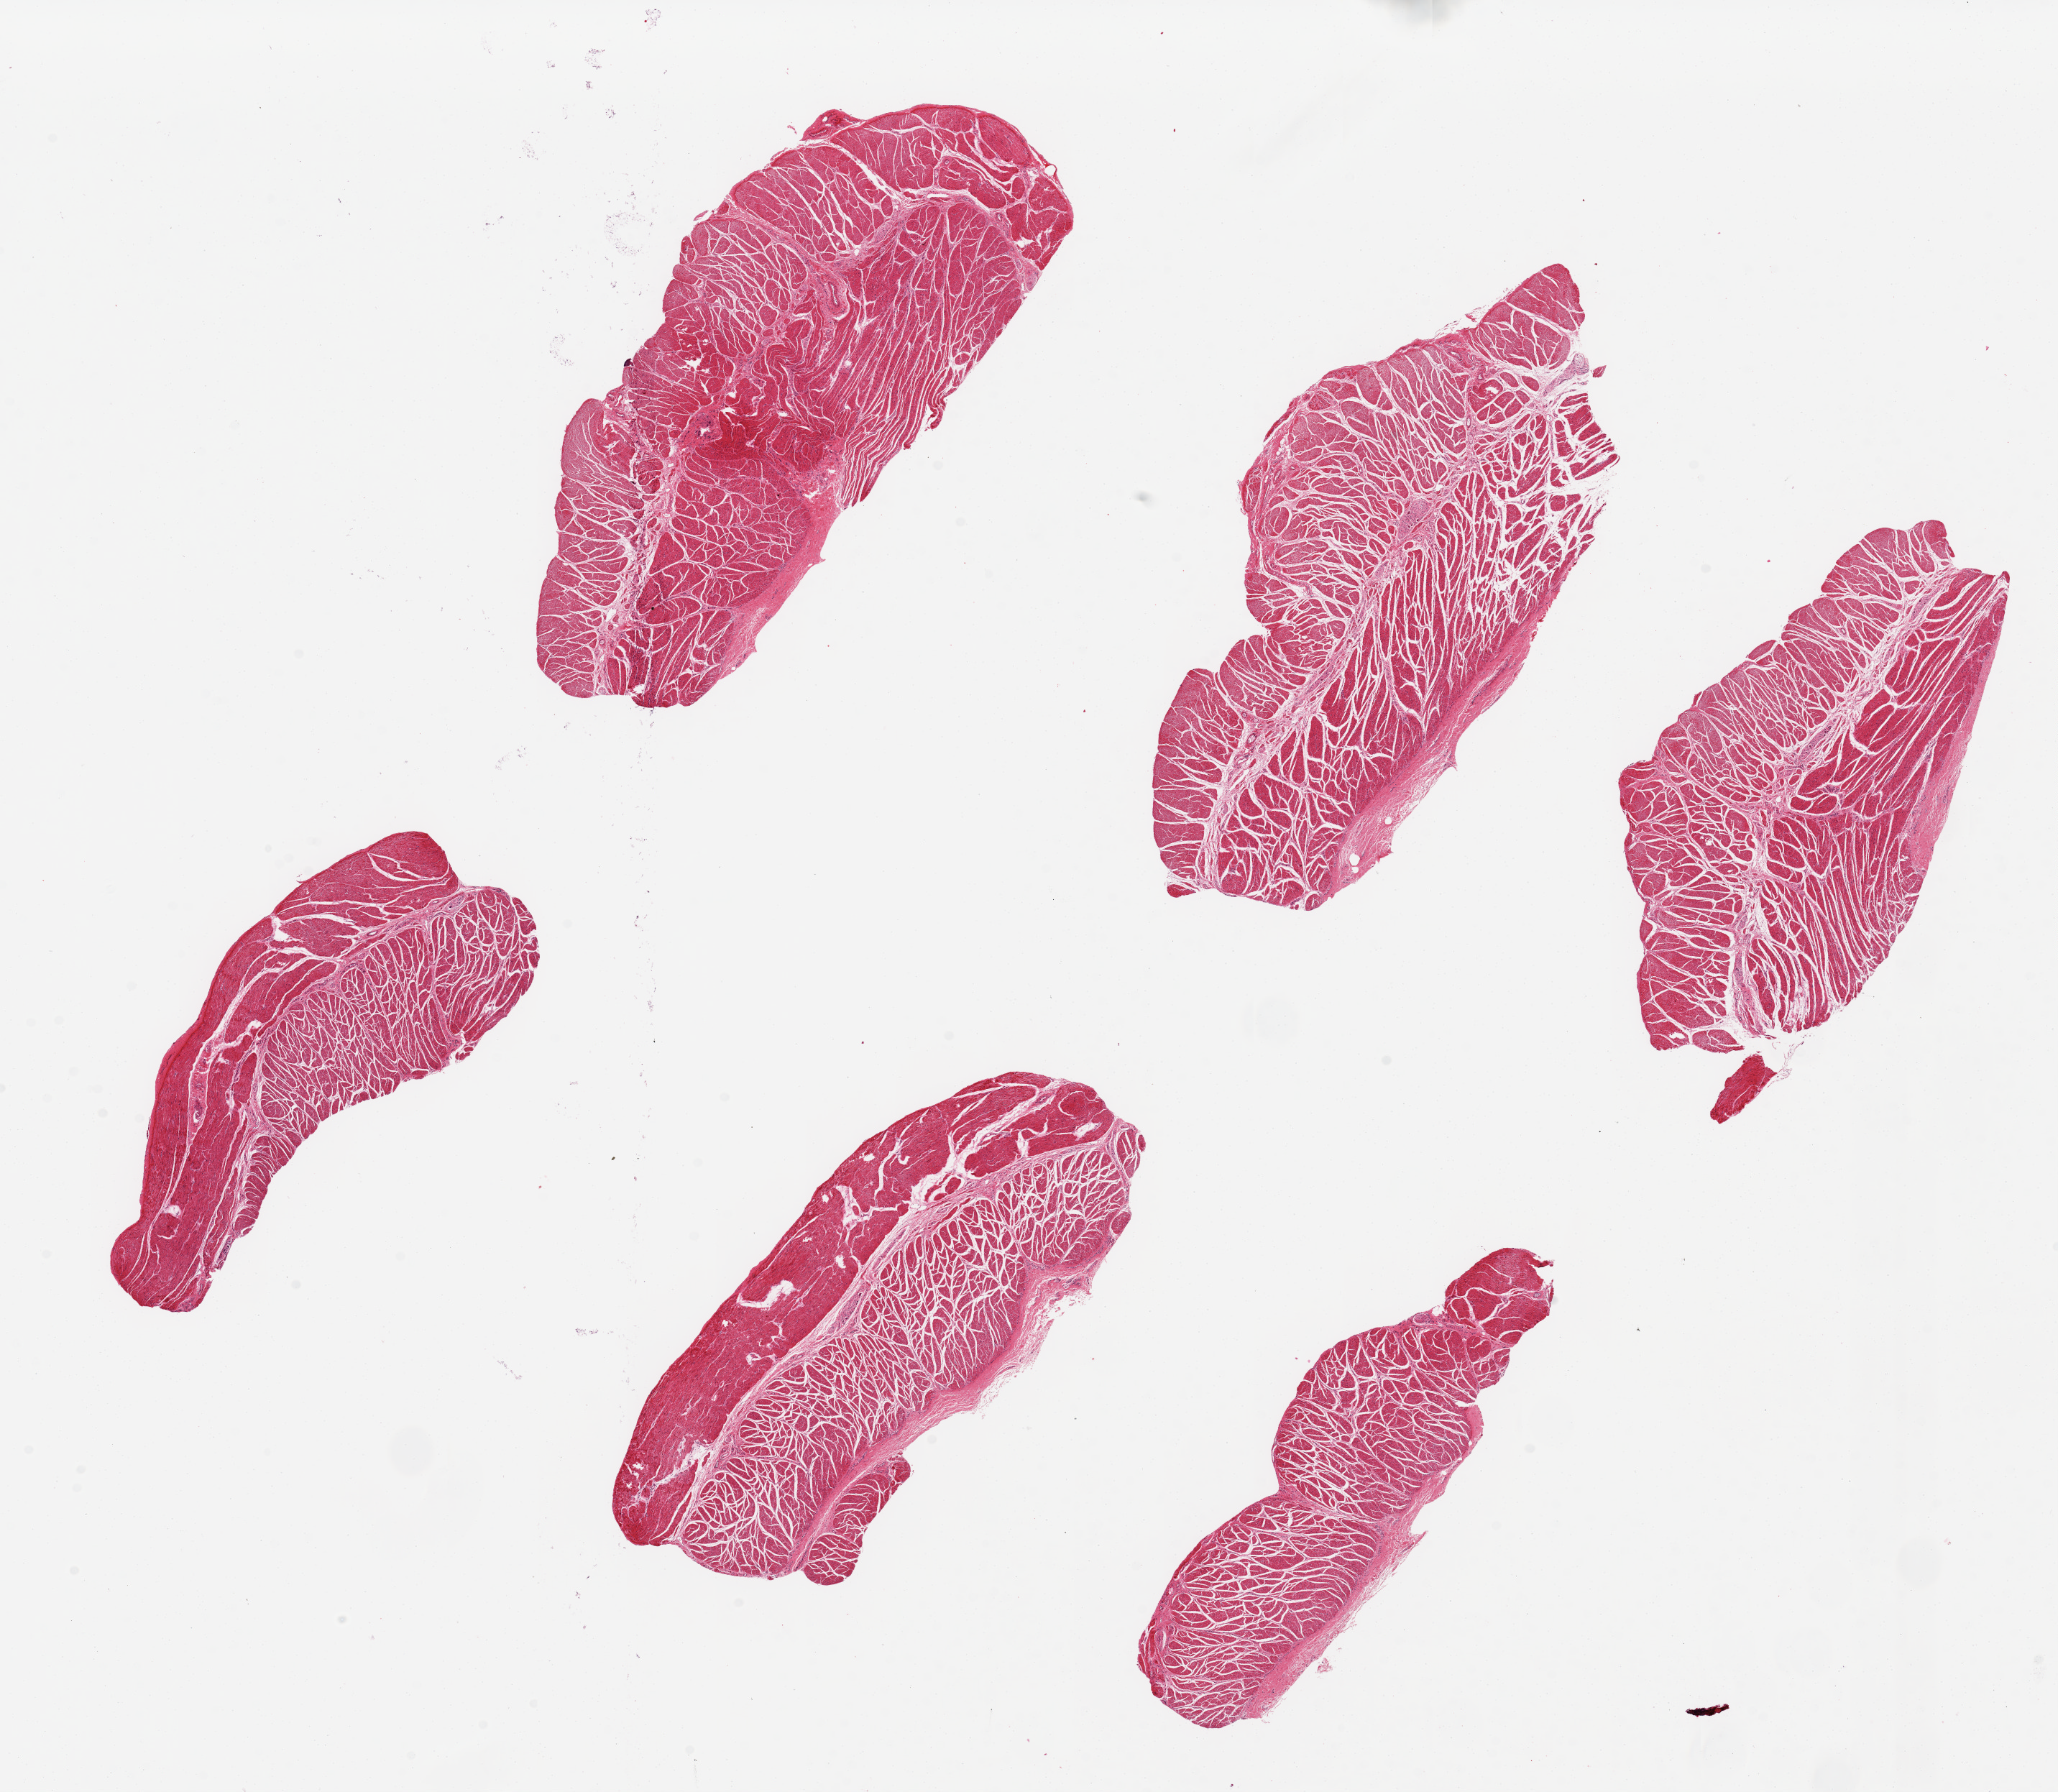
Digitized haematoxylin and eosin-stained section, whole scanned area (about 22.6 x 19.7 mm, from a 20x scan) shown as a low-resolution overview. PAXgene-fixed paraffin-embedded (PFPE) section. Sampled site (target tissue): esophageal muscle. Tissue donor sample. Male donor.
Pathologist's review note for this sample: 6 pieces up to 7.7x3.4 mm.